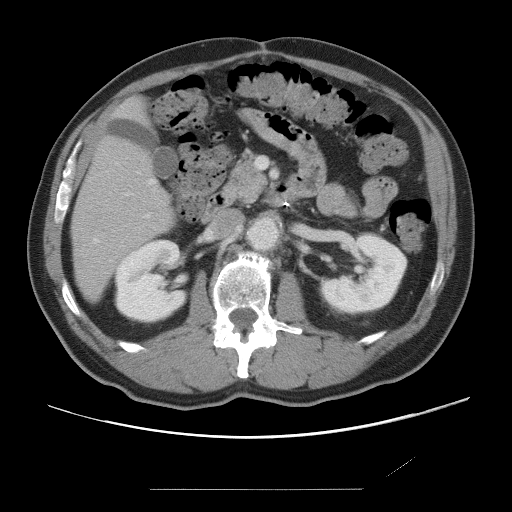
Contrast-enhanced abdominal CT, one axial slice; position 28 of 87 along the scan axis; intravenous contrast given; soft-tissue window (W 400 / L 40 HU); 512 × 512 image matrix, field of view 406 × 406 mm. Male patient, age 74 years. Case-level facts recorded for this patient, not image findings: diagnosis: colorectal cancer liver metastases, imaged before liver resection; multiple liver metastases: yes; largest metastasis: 1.1 cm; disease in both lobes: no.
Structures marked on this image (outlined manually by an expert reader):
- hepatic veins: box from (x=94, y=179) to (x=155, y=243) px
- liver: (x=71, y=101)–(x=175, y=300)
- planned liver remnant (the part of the liver to remain after resection): (x=71, y=101)–(x=176, y=299)
- portal vein (with intrahepatic branches): (x=138, y=172)–(x=150, y=218)